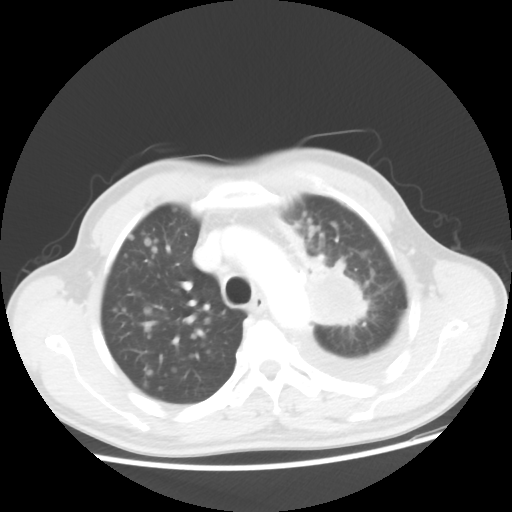
Chest CT, one axial slice; slice 36 of 48 in the series (ordered by position); 100 kVp; lung window (W 1500 / L -600 HU); 5 mm slice thickness; 512 × 512 image matrix. Male patient, age 55 years. Case-level facts recorded for this patient, not image findings: clinical TNM (as recorded): T2 N3 M1a; histopathological grade: G3.
Annotated regions visible in this slice (rectangle marked by the reading radiologist):
- lung tumour (recorded histology: squamous cell carcinoma): bounding box <301,259,378,334> (left, top, right, bottom; pixels)